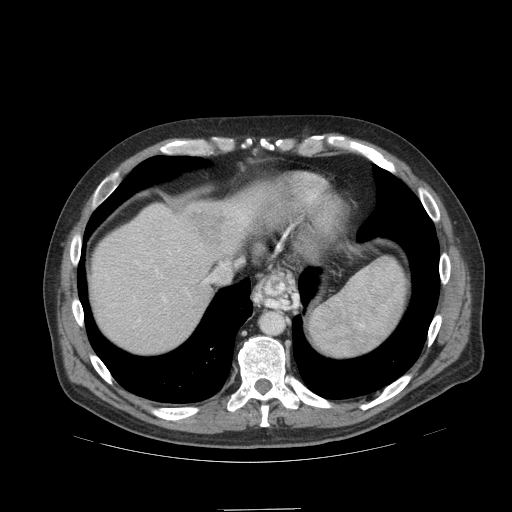
Contrast-enhanced abdominal CT (liver protocol), one axial slice; position 87 of 99 along the scan axis; reconstruction kernel STANDARD; 140 kVp; soft-tissue window (W 400 / L 40 HU); 2.5 mm slice thickness; 512 × 512 image matrix, field of view 440 × 440 mm. Case-level facts recorded for this patient, not image findings: diagnosis: hepatocellular carcinoma (patient treated with transarterial chemoembolisation; whether this scan precedes or follows treatment is not stated here); TNM stage (as recorded): Stage-I; Child-Pugh class: A; tumour size: 3.6 cm.
Annotated regions visible in this slice (semi-automatically segmented with operator editing):
- abdominal aorta: bounding box <261,313,283,333> (left, top, right, bottom; pixels)
- liver parenchyma outside the tumour (the mass and vessels are separate outlines, so this box may not span the whole liver): <90,188,264,352>
- mass: <187,209,223,248>
- liver vessels: <107,210,244,322>